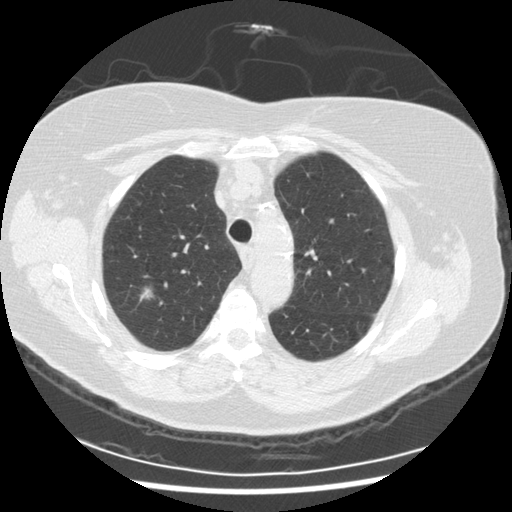
Low-dose screening chest CT, axial slice. Third screening round (two years after baseline). Lung window (W 1500 / L -600 HU). 2.5 mm slice thickness. 512 × 512 image matrix, field of view 360 × 360 mm. Female participant, aged 72 years at enrolment.
Expert-annotated lung lesion, bounding box (x1, y1, x2, y2) in pixels: (129, 280, 162, 310). Screening reader's record for this exam (one nodule recorded; not confirmed to be the boxed lesion): non-calcified nodule or mass ≥4 mm, right upper lobe, 9 × 8 mm, poorly defined margins, ground glass attenuation, pre-existing on the prior screen: no. Official screen result: positive, other.